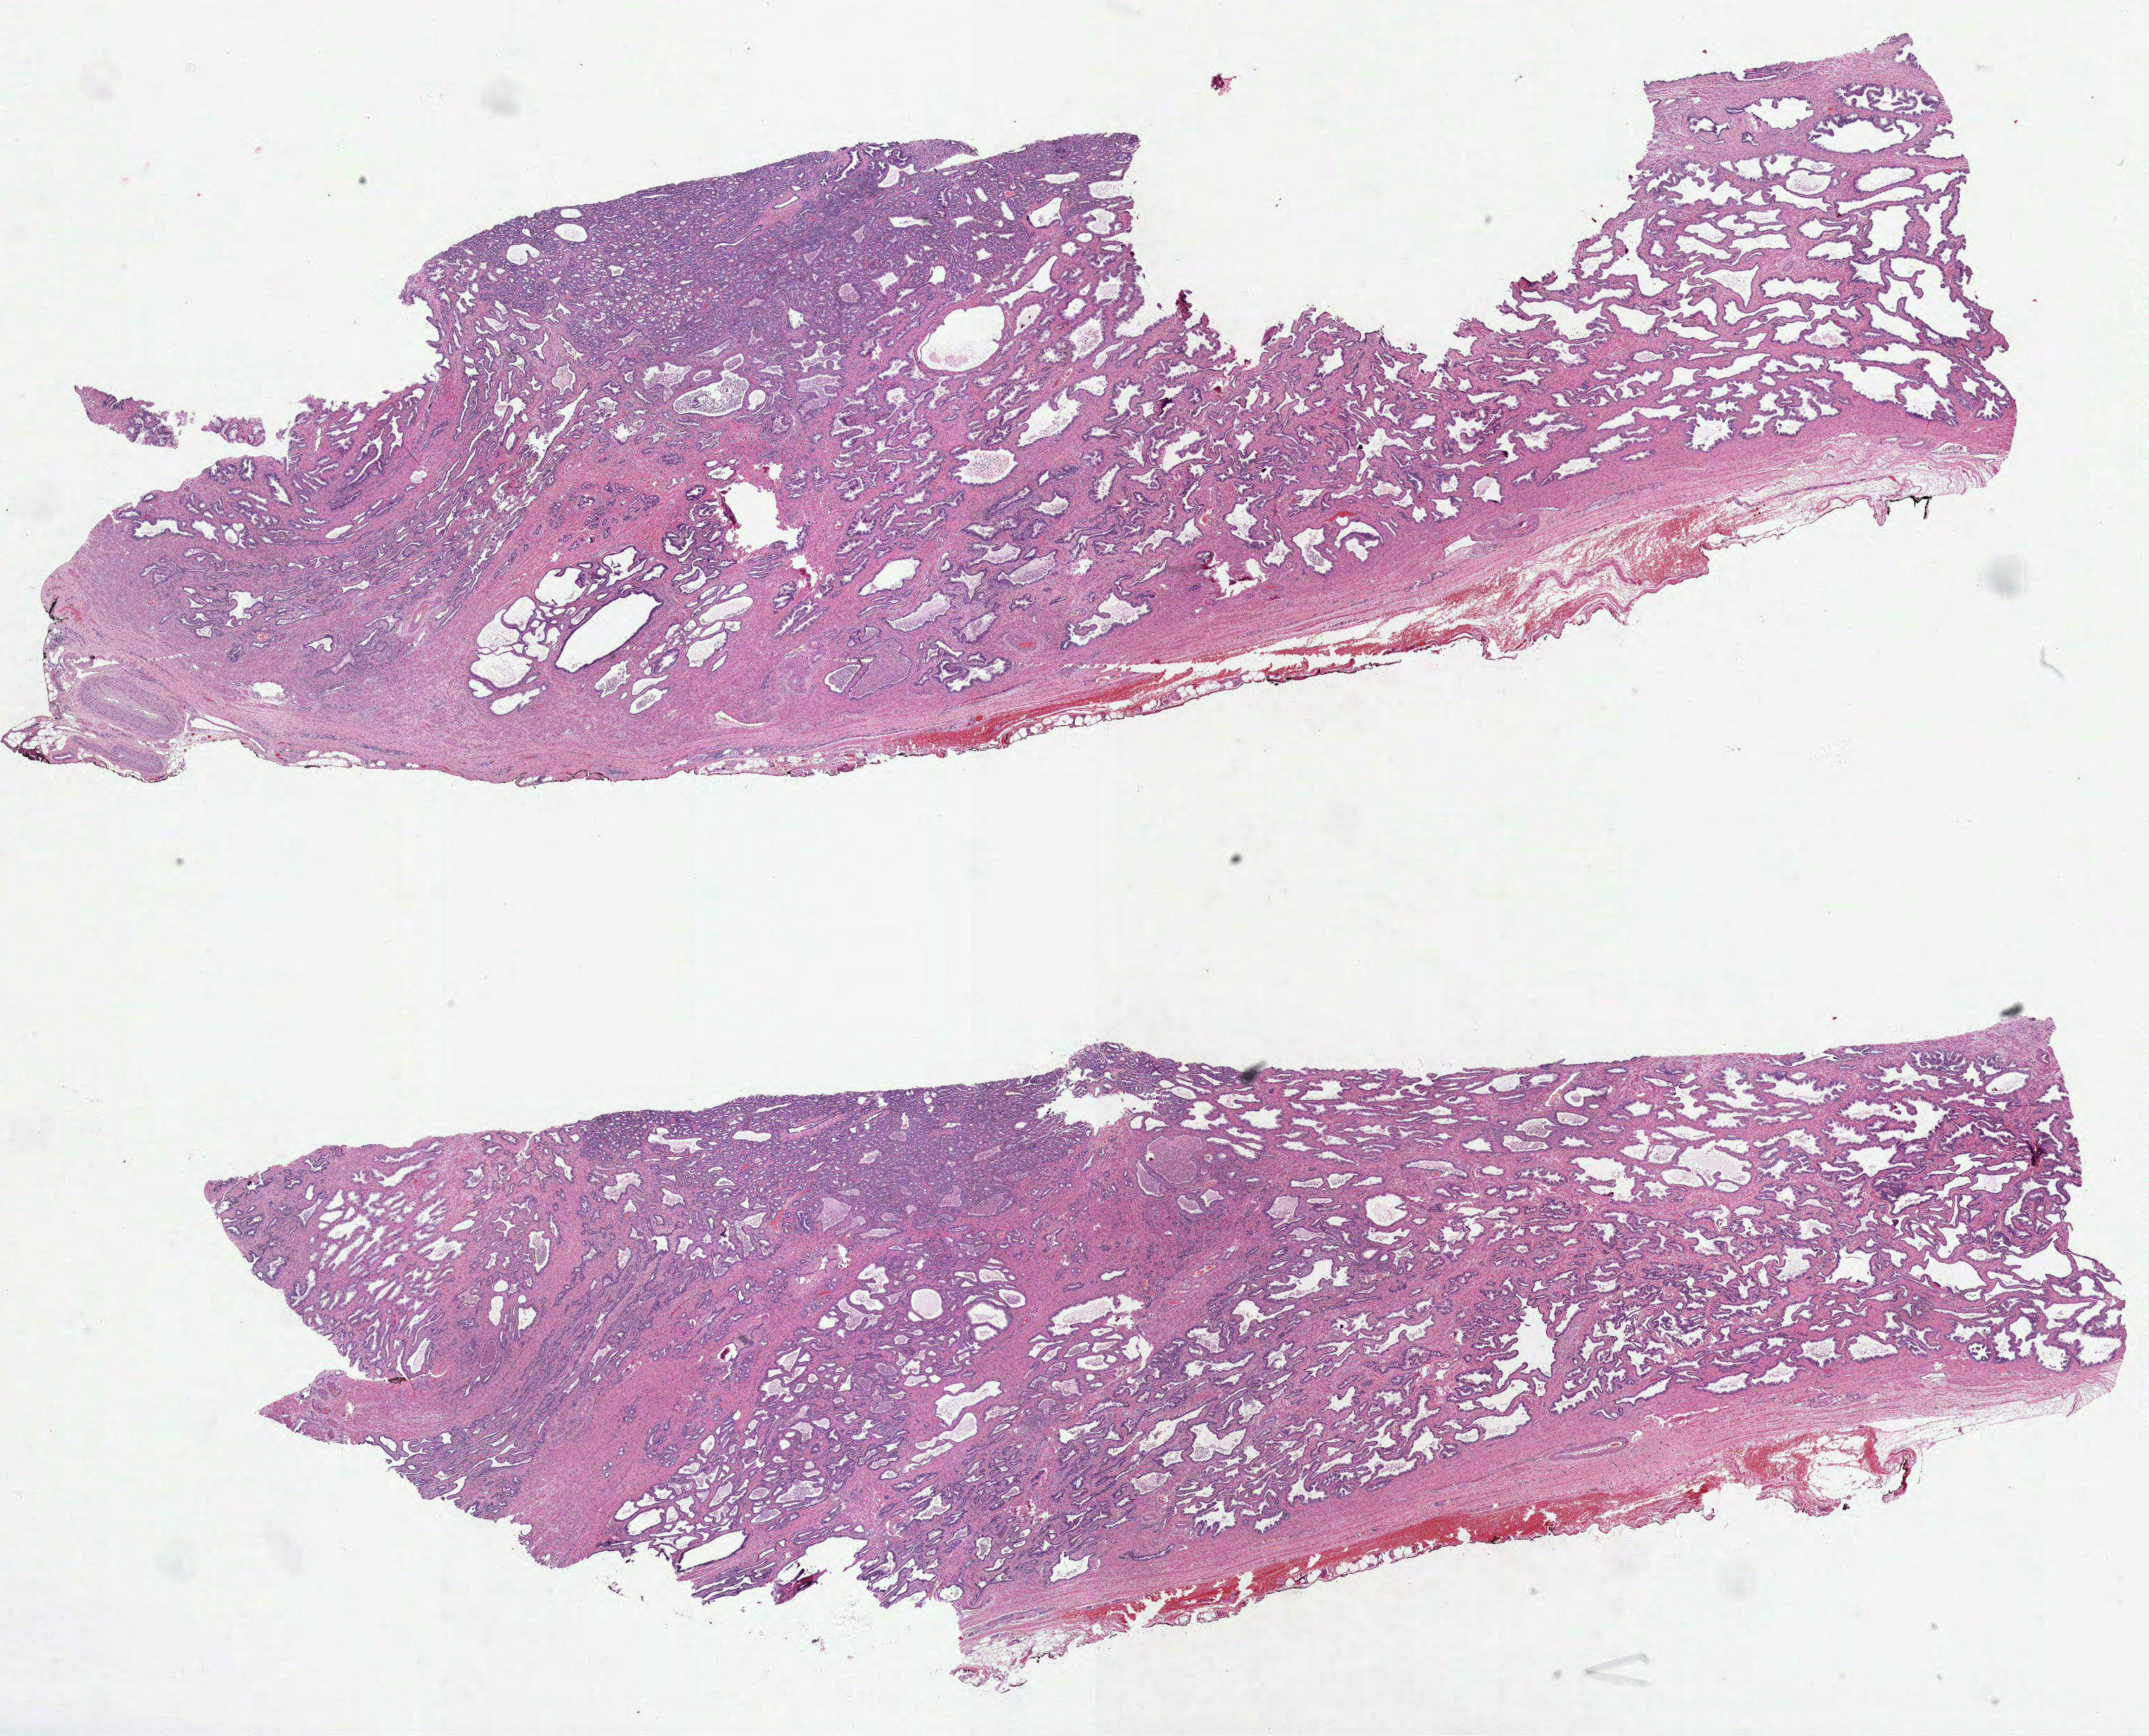
H&E whole-slide image, low-resolution overview of the scanned area, about 24.7 x 19.9 mm (slide scanned at 40x). Formalin-fixed paraffin-embedded (FFPE) diagnostic section. Sample: primary tumour, prostate. Patient: male, age at initial diagnosis 53 years. Gleason score: 7 (3+4).
* lymph nodes positive (case pathology): 0 of 14 examined
* pathologic diagnosis: Acinar cell carcinoma